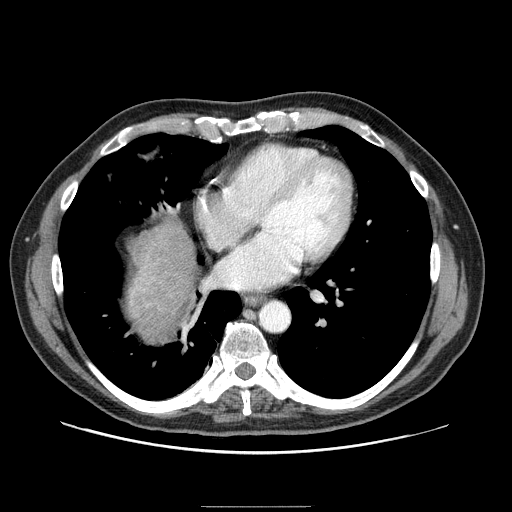
Contrast-enhanced abdominal CT (liver protocol), one axial slice; slice 88 of 99 in the series (ordered by position); reconstruction kernel STANDARD; 100 kVp; one of 2 acquisitions stored at this slice position; soft-tissue window (W 400 / L 40 HU); 2.5 mm slice thickness; 512 × 512 image matrix, field of view 400 × 400 mm. From the clinical record (not read from this slice): diagnosis: hepatocellular carcinoma (patient treated with transarterial chemoembolisation; whether this scan precedes or follows treatment is not stated here); TNM stage (as recorded): Stage-II; Child-Pugh class: A; tumour size: 3.2 cm.
Outlined on this slice (semi-automatically segmented with operator editing):
- liver parenchyma outside the tumour (the mass and vessels are separate outlines, so this box may not span the whole liver): box from (x=128, y=218) to (x=196, y=338) px